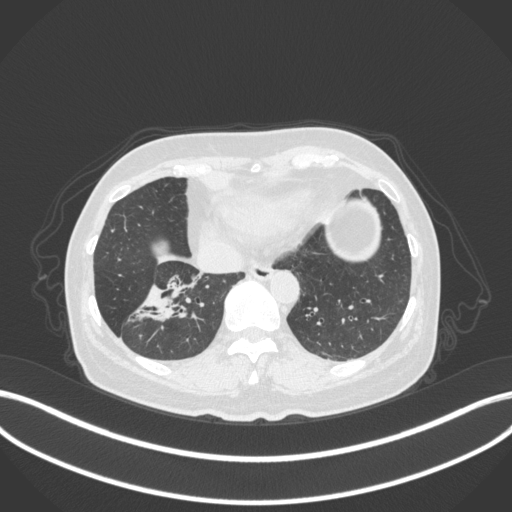
Chest CT, one axial slice. Position 111 of 429 along the scan axis. Lung window (W 1500 / L -600 HU). 1 mm slice thickness. 512 × 512 image matrix, field of view 400 × 400 mm. Female patient, age 67 years. Case-level facts recorded for this patient, not image findings: clinical TNM (as recorded): T1c N1 M0; histopathological grade: G2-3.
Outlined on this slice (bounding box drawn by a radiologist):
- lung tumour (recorded histology: adenocarcinoma): bounding box <132,263,208,329> (left, top, right, bottom; pixels)